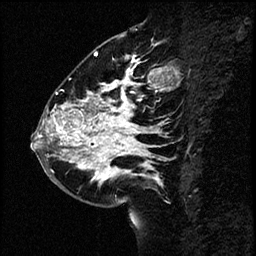
Breast MRI (dynamic contrast-enhanced), one sagittal slice. Dynamic contrast-enhanced study with each time point stored as its own series, time point 2 of 4 at this slice position (early post-contrast, ordered by acquisition time). 1.5 T. TE 4.2 ms, TR 17.6 ms. 2 mm slice thickness. 256 × 256 image matrix, field of view 200 × 200 mm. Patient: female, 43 years. From the clinical record (not read from this slice): setting: breast cancer imaged before/during neoadjuvant chemotherapy.
Outlined on this slice (semi-automatically segmented with operator editing):
- analysis volume of interest (the breast-tissue region the enhancement analysis was run in; not a lesion): bounding box [x1, y1, x2, y2] px = [34, 56, 169, 191]
- tumour enhancement mask (voxels above the 100 % enhancement threshold inside the analysis volume of interest): [36, 56, 154, 179]